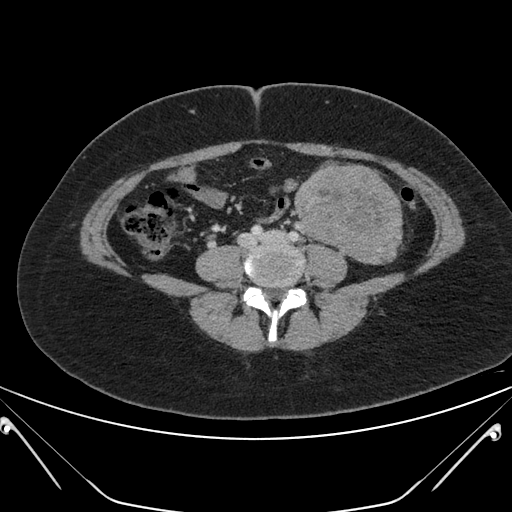
Contrast-enhanced abdominal CT, one axial slice; slice 74 of 168 in the series (ordered by position); 120 kVp; intravenous contrast given; soft-tissue window (W 400 / L 40 HU); 512 × 512 image matrix, field of view 394 × 394 mm. Patient: female, 26 years. Case-level facts recorded for this patient, not image findings: diagnosis: adrenocortical carcinoma; tumour side: left adrenal.
Annotated regions visible in this slice (semi-automatic segmentation, software-assisted and operator-edited):
- mass: bounding box <297,167,400,263> (left, top, right, bottom; pixels)